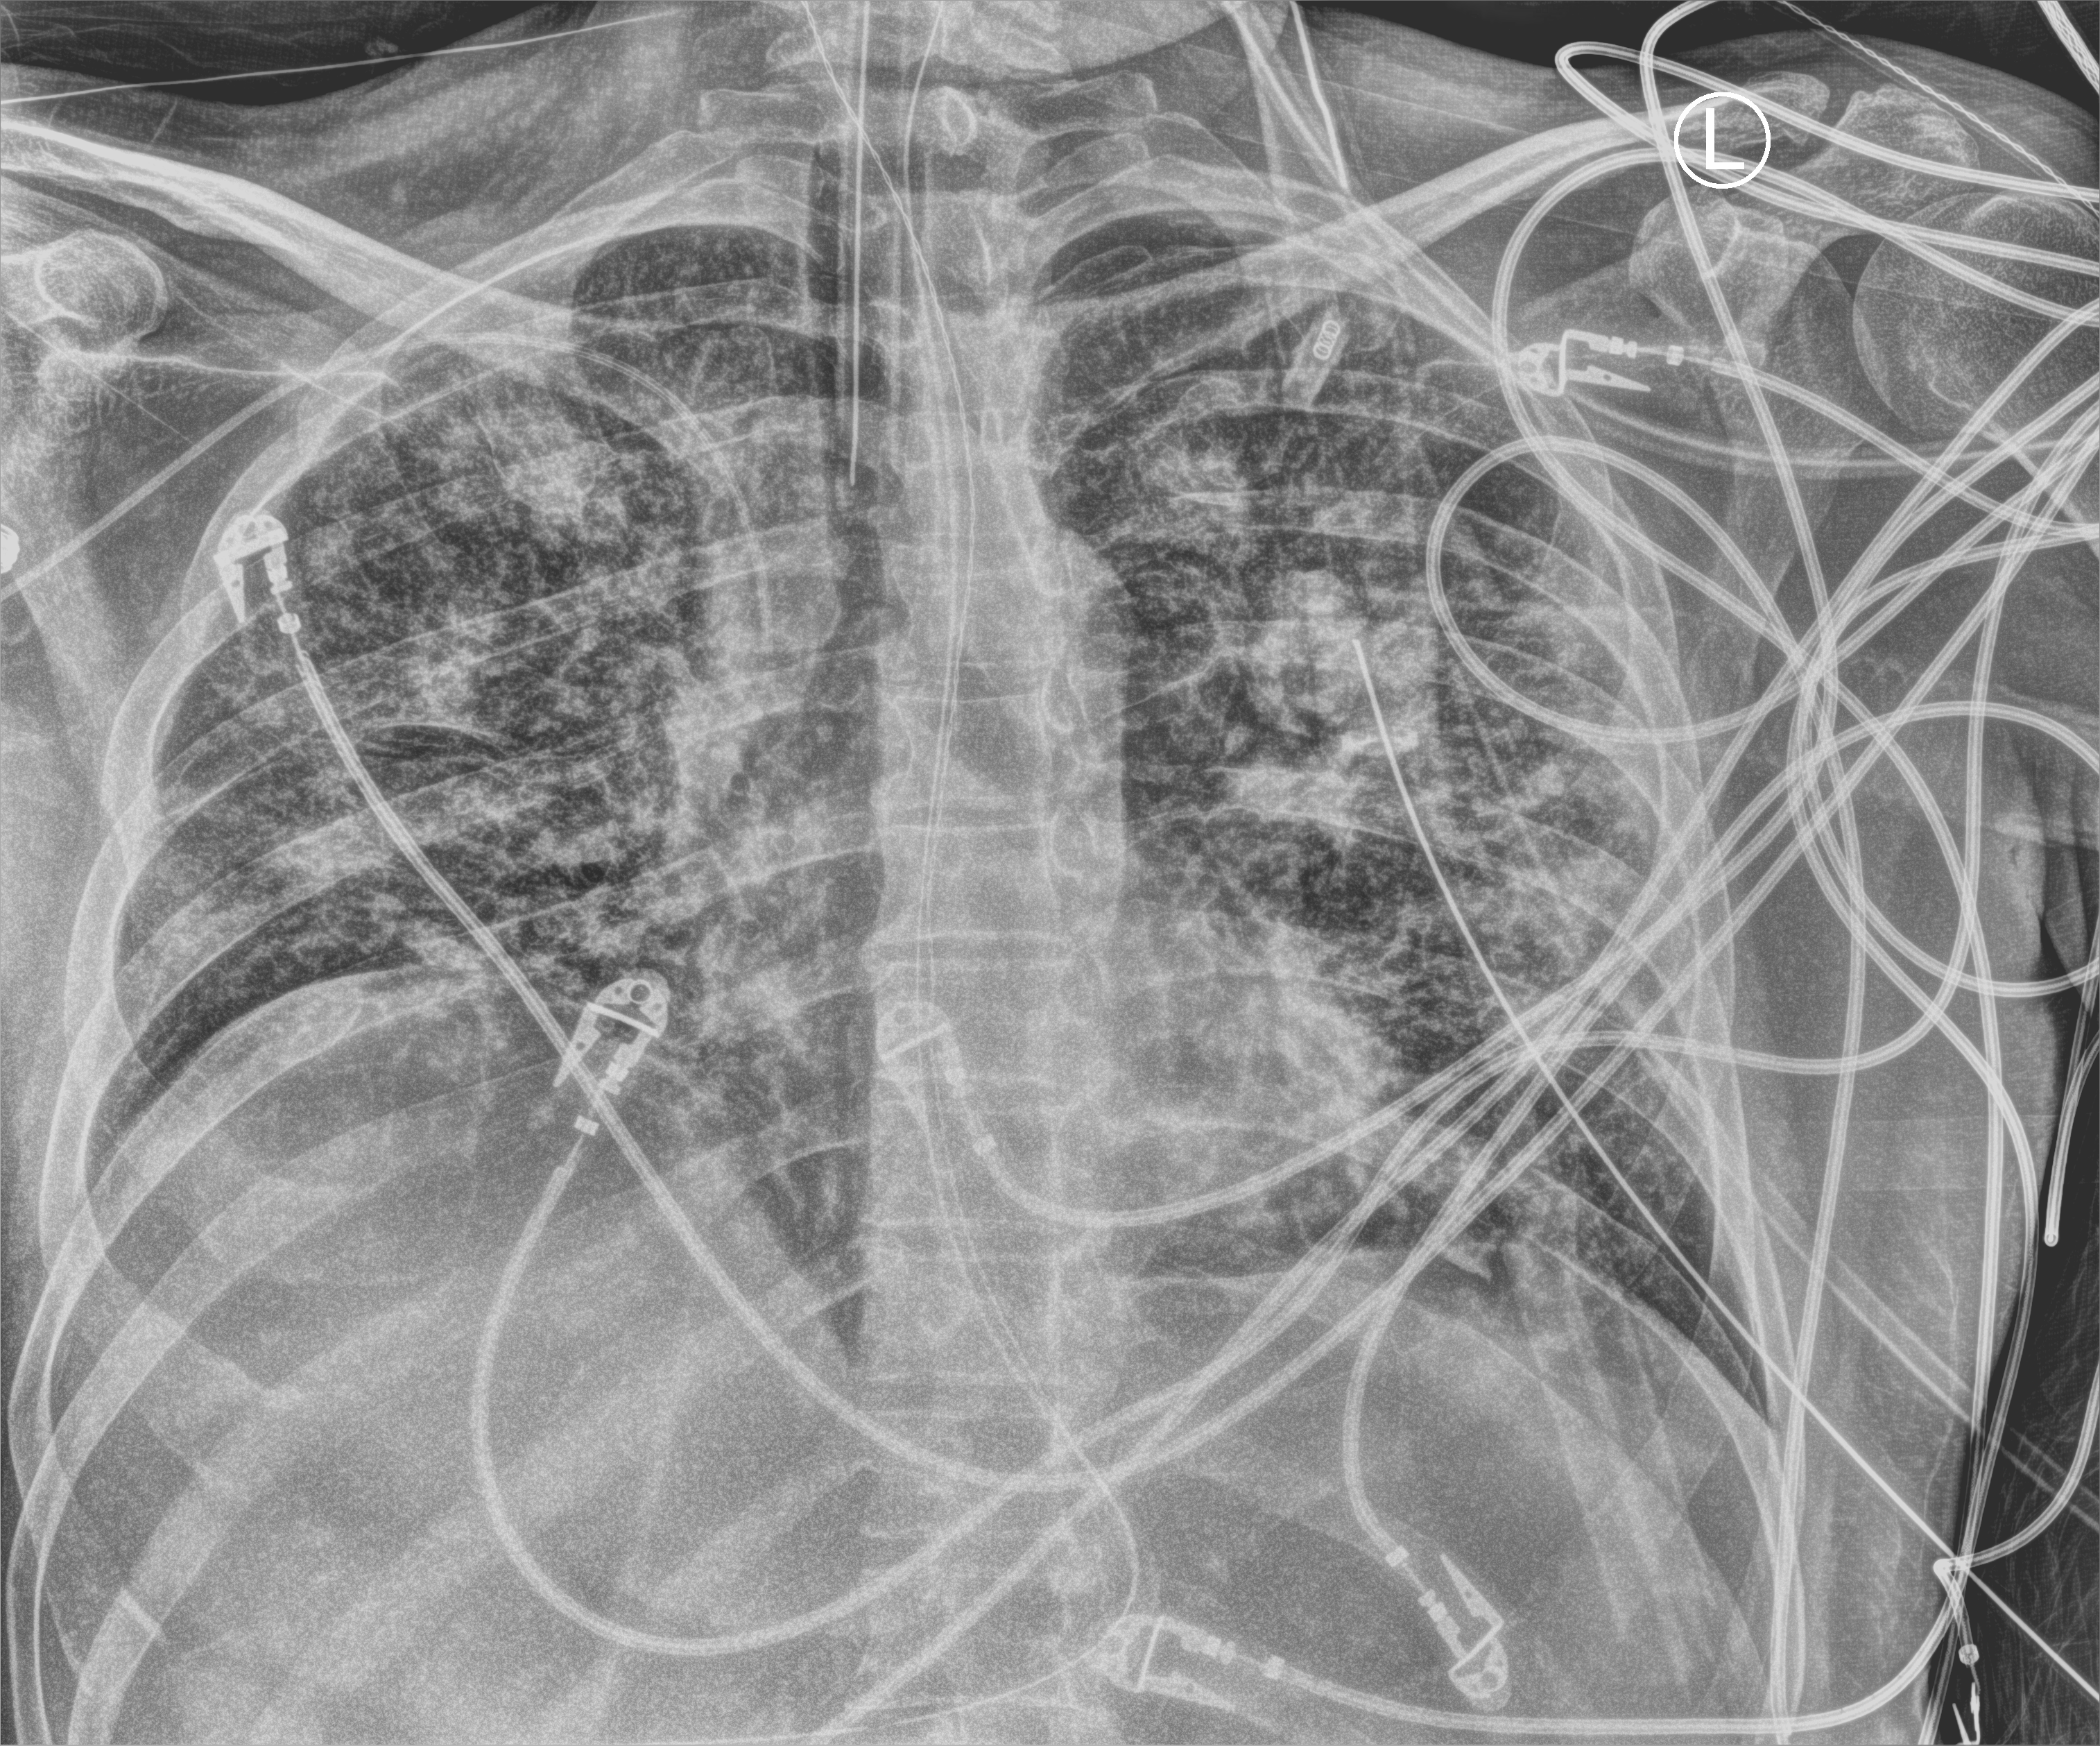
Portable chest radiograph; anteroposterior (AP) projection. Patient hospitalised with COVID-19; male, aged 18–59 years.
Hospital-stay facts (about this admission, not read from this image; timing relative to this image not recorded): mechanically ventilated during this hospital stay: yes; admitted to intensive care during this hospital stay: yes; chronic kidney disease (admission record): no.